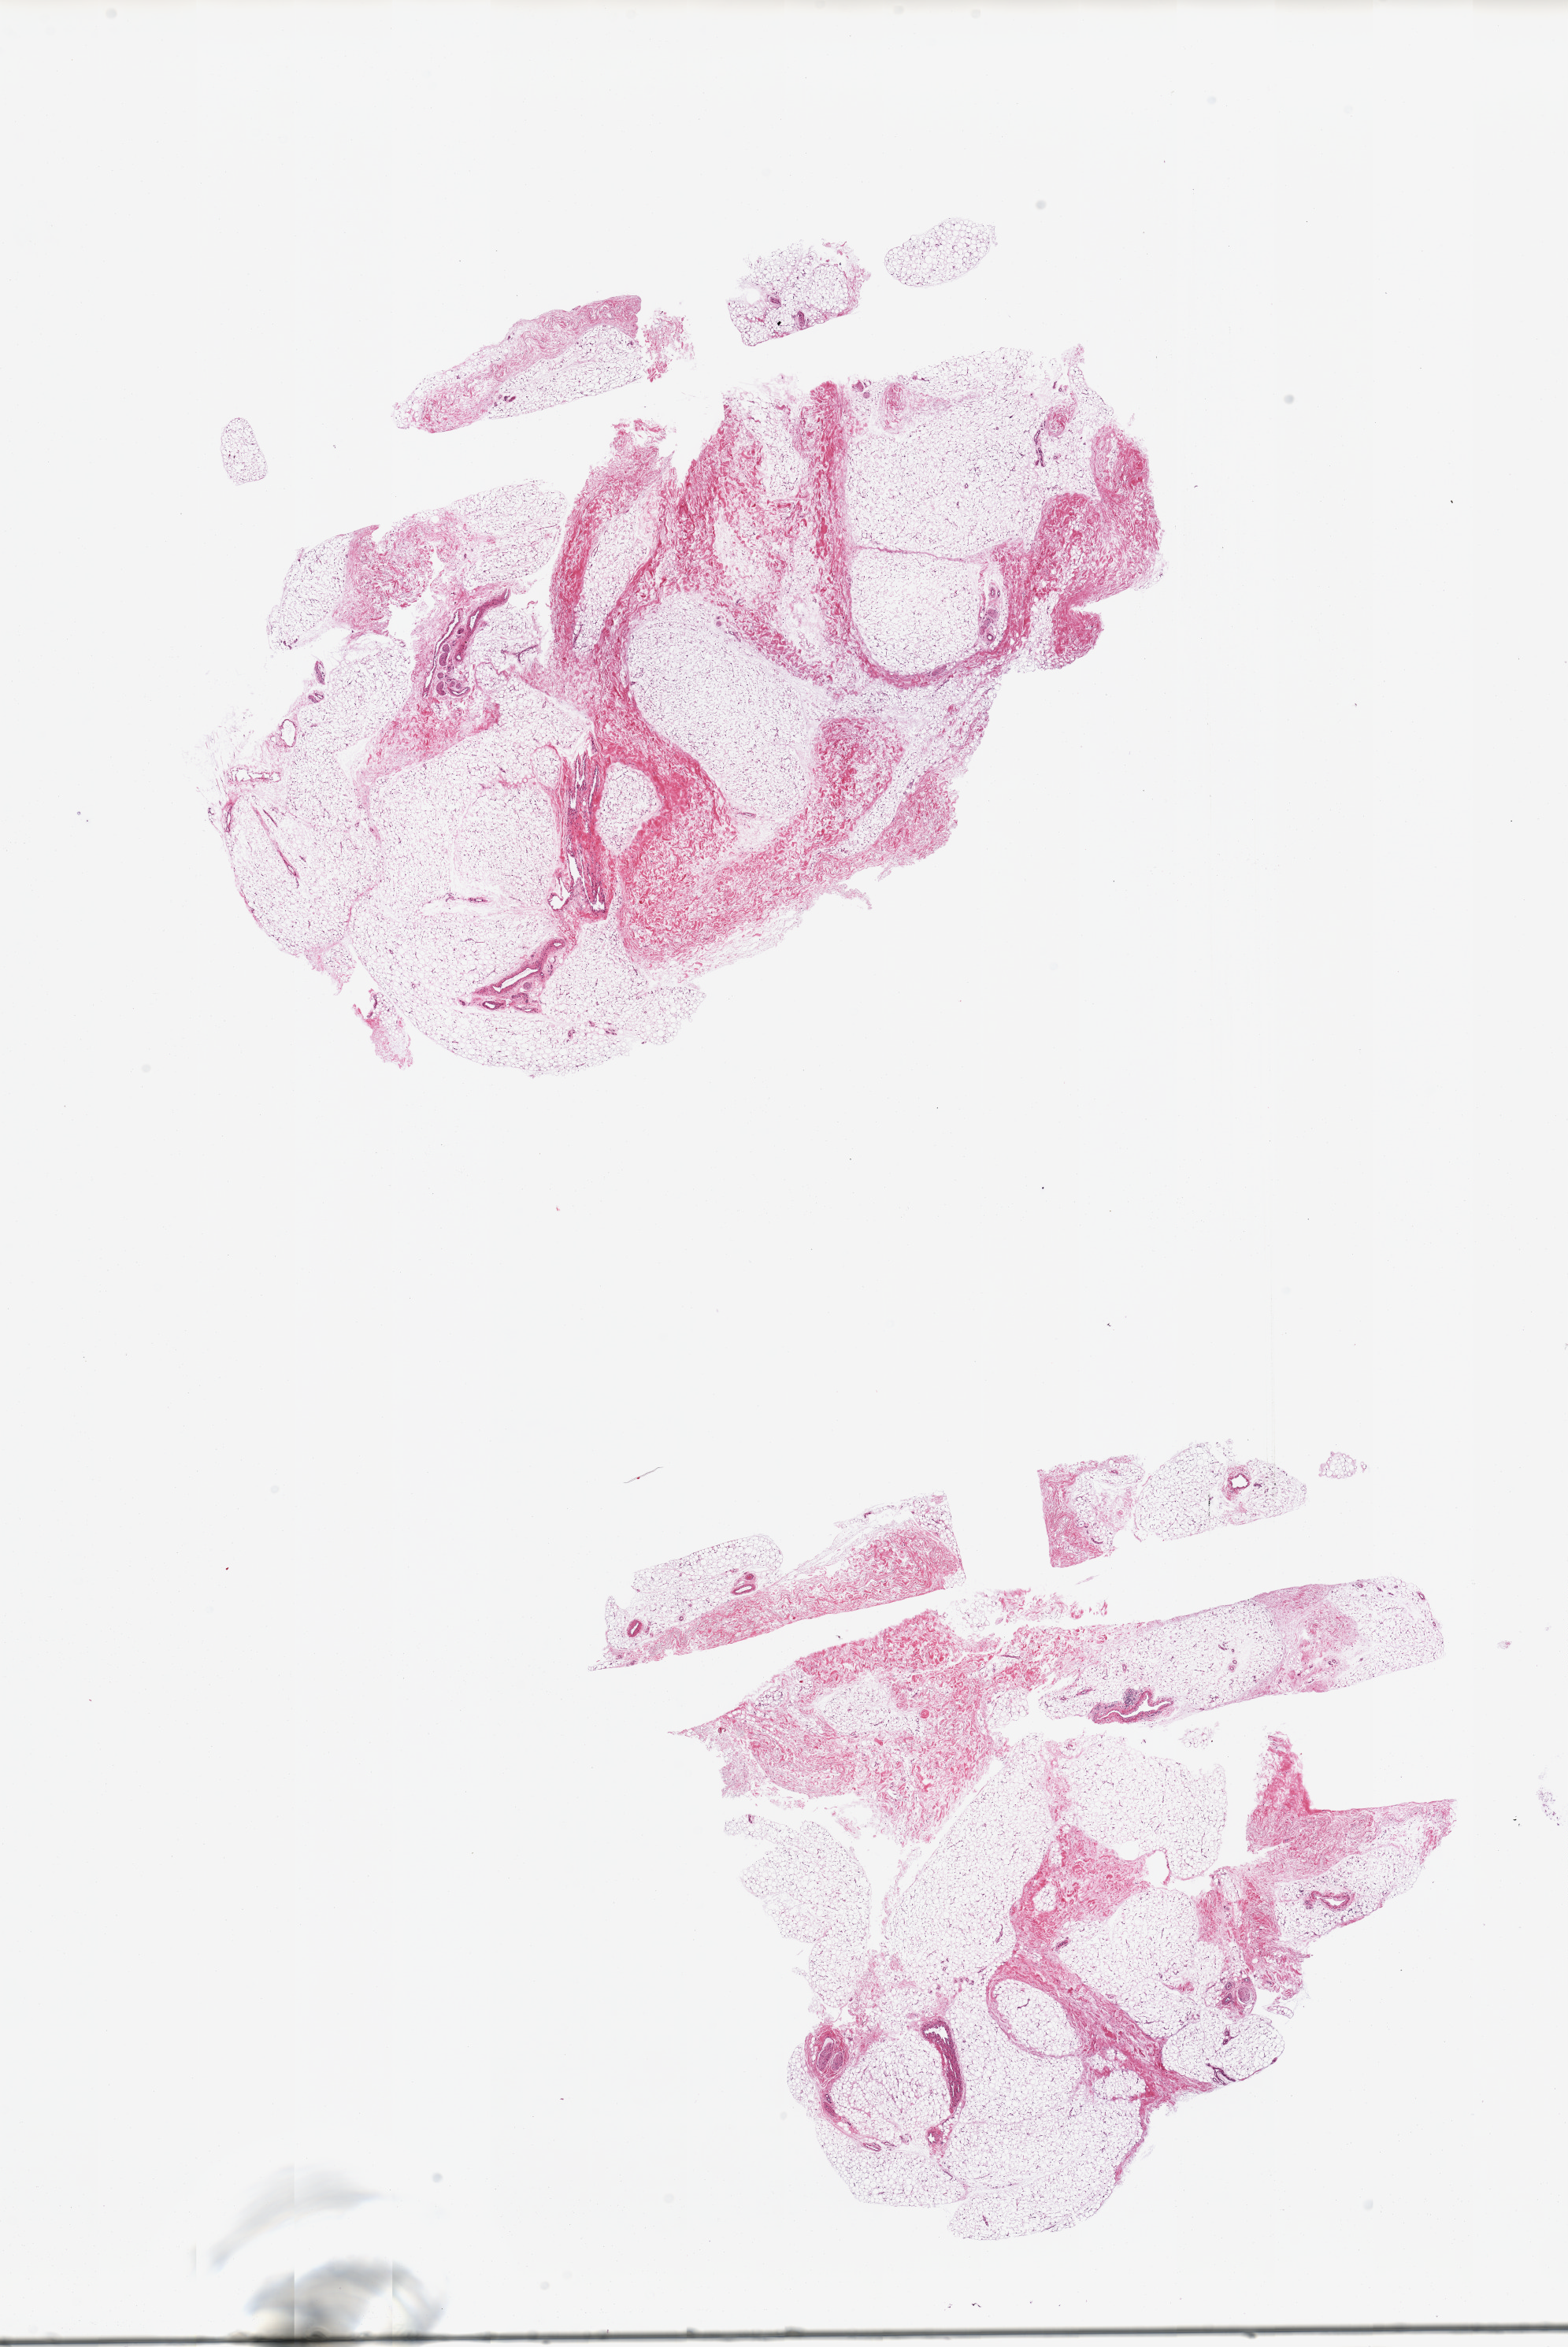
Whole-slide image, hematoxylin and eosin (H&E) stain, low-resolution overview of the scanned area, about 15.8 x 23.6 mm (acquisition: 20x scan), PAXgene-fixed, paraffin-embedded tissue, sampled site (target tissue): adipose tissue, tissue donor sample. Male donor.
Review note (as recorded): 2 pieces; mature adipose with ~25% fibrovascular component and nerves.